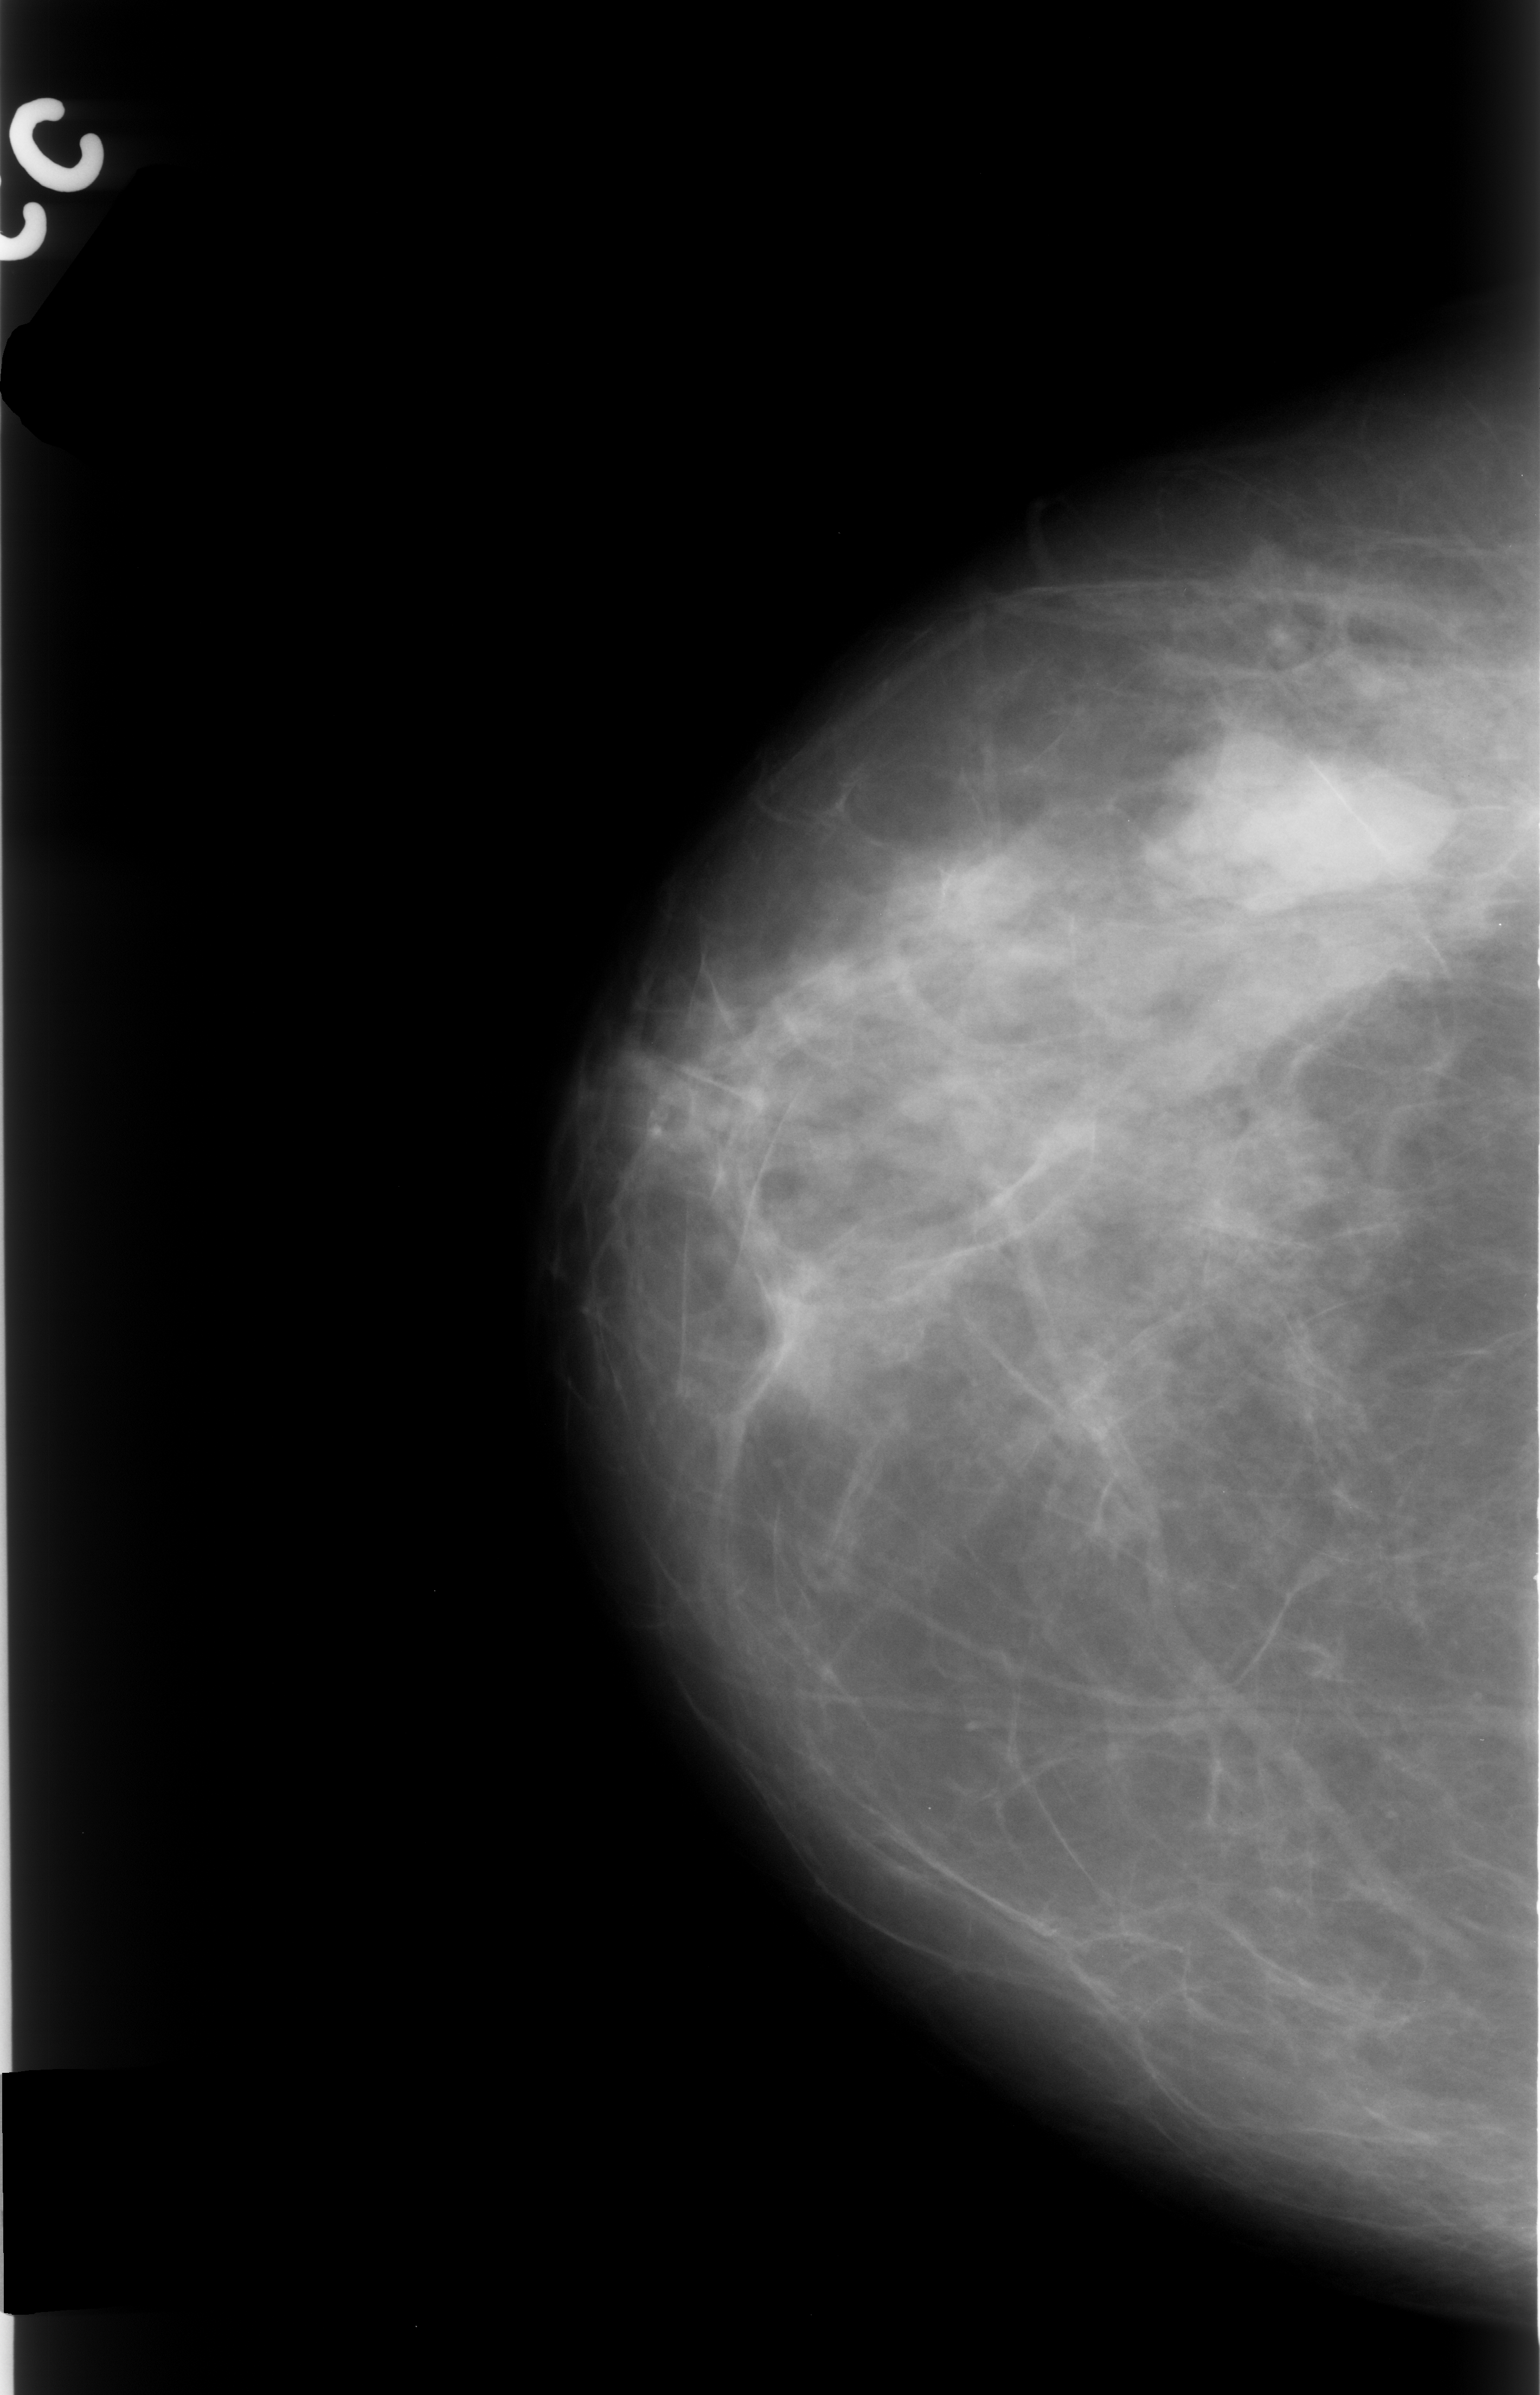
Mammogram (digitized film), right breast, craniocaudal (CC) view, breast composition: scattered fibroglandular densities (BI-RADS density category 2 of 4).
- Marked findings (only marked abnormalities are described; nothing is implied about the rest of the image): mass, shape lobulated, margins circumscribed; BI-RADS assessment category 4; subtlety rating 5 on a 1 (subtle) to 5 (obvious) scale; pathology result (as recorded, not read from the image): benign.